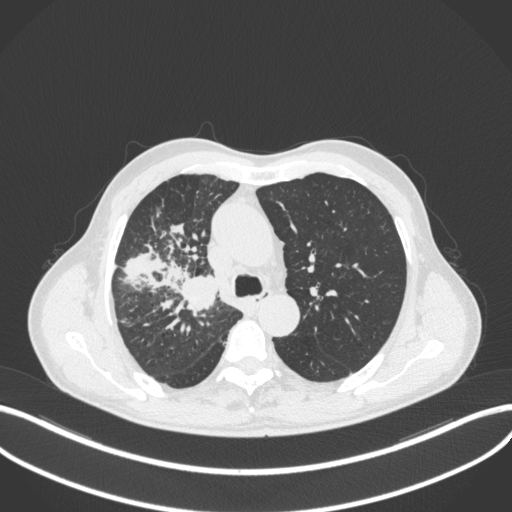
Chest CT, one axial slice; slice 334 of 490 in the series (ordered by position); reconstruction kernel B31f; 120 kVp; lung window (W 1500 / L -600 HU); 1 mm slice thickness; 512 × 512 image matrix. Male patient, age 69 years. Case-level facts recorded for this patient, not image findings: clinical TNM (as recorded): T2a N0 M0.
Outlined on this slice (rectangle marked by the reading radiologist):
- lung tumour (recorded histology: adenocarcinoma): bounding box (x1, y1, x2, y2) in pixels: (179, 271, 224, 317)